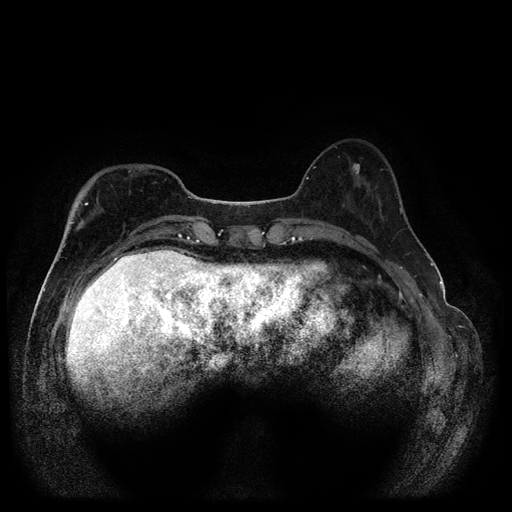
Breast MRI (dynamic contrast-enhanced, multi-phase), one axial slice; position 34 of 116 along the scan axis; dynamic contrast-enhanced series, time point 2 of 5 at this slice position (early post-contrast); 1.5 T; TE 2.6 ms, TR 5.4 ms; 2 mm slice thickness; 512 × 512 image matrix. Patient: female, 51 years.
Annotated regions visible in this slice (semi-automatically segmented with operator editing):
- breast lesion (labelled benign in the annotation): box from (x=352, y=163) to (x=361, y=176) px